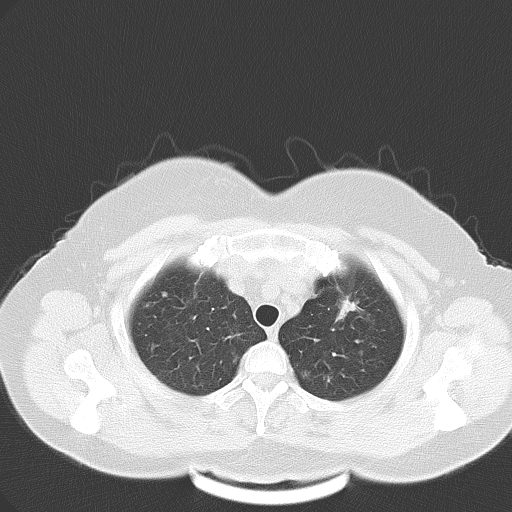
Chest CT, one axial slice. Position 46 of 57 along the scan axis. 120 kVp. Lung window (W 1500 / L -600 HU). 512 × 512 image matrix. Patient: female, 53 years. Case-level facts recorded for this patient, not image findings: clinical TNM (as recorded): T1c N0 M1a.
Annotated regions visible in this slice (bounding box drawn by a radiologist):
- lung tumour (recorded histology: adenocarcinoma): box from (x=330, y=296) to (x=358, y=321) px